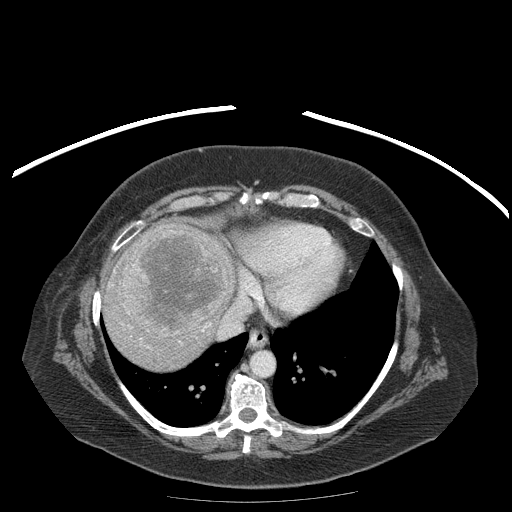
Contrast-enhanced abdominal CT (liver protocol), one axial slice; slice 161 of 204 in the series (ordered by position); reconstruction kernel STANDARD; soft-tissue window (W 400 / L 40 HU); 512 × 512 image matrix. Case-level facts recorded for this patient, not image findings: diagnosis: hepatocellular carcinoma (patient treated with transarterial chemoembolisation; whether this scan precedes or follows treatment is not stated here); TNM stage (as recorded): Stage-IIIB; Child-Pugh class: A; tumour differentiation: well differentiated; tumour nodularity: uninodular.
Structures marked on this image (semi-automatic segmentation, software-assisted and operator-edited):
- liver parenchyma outside the tumour (the mass and vessels are separate outlines, so this box may not span the whole liver): bounding box <104,222,234,370> (left, top, right, bottom; pixels)
- mass: <117,225,229,338>
- liver vessels: <114,271,211,331>